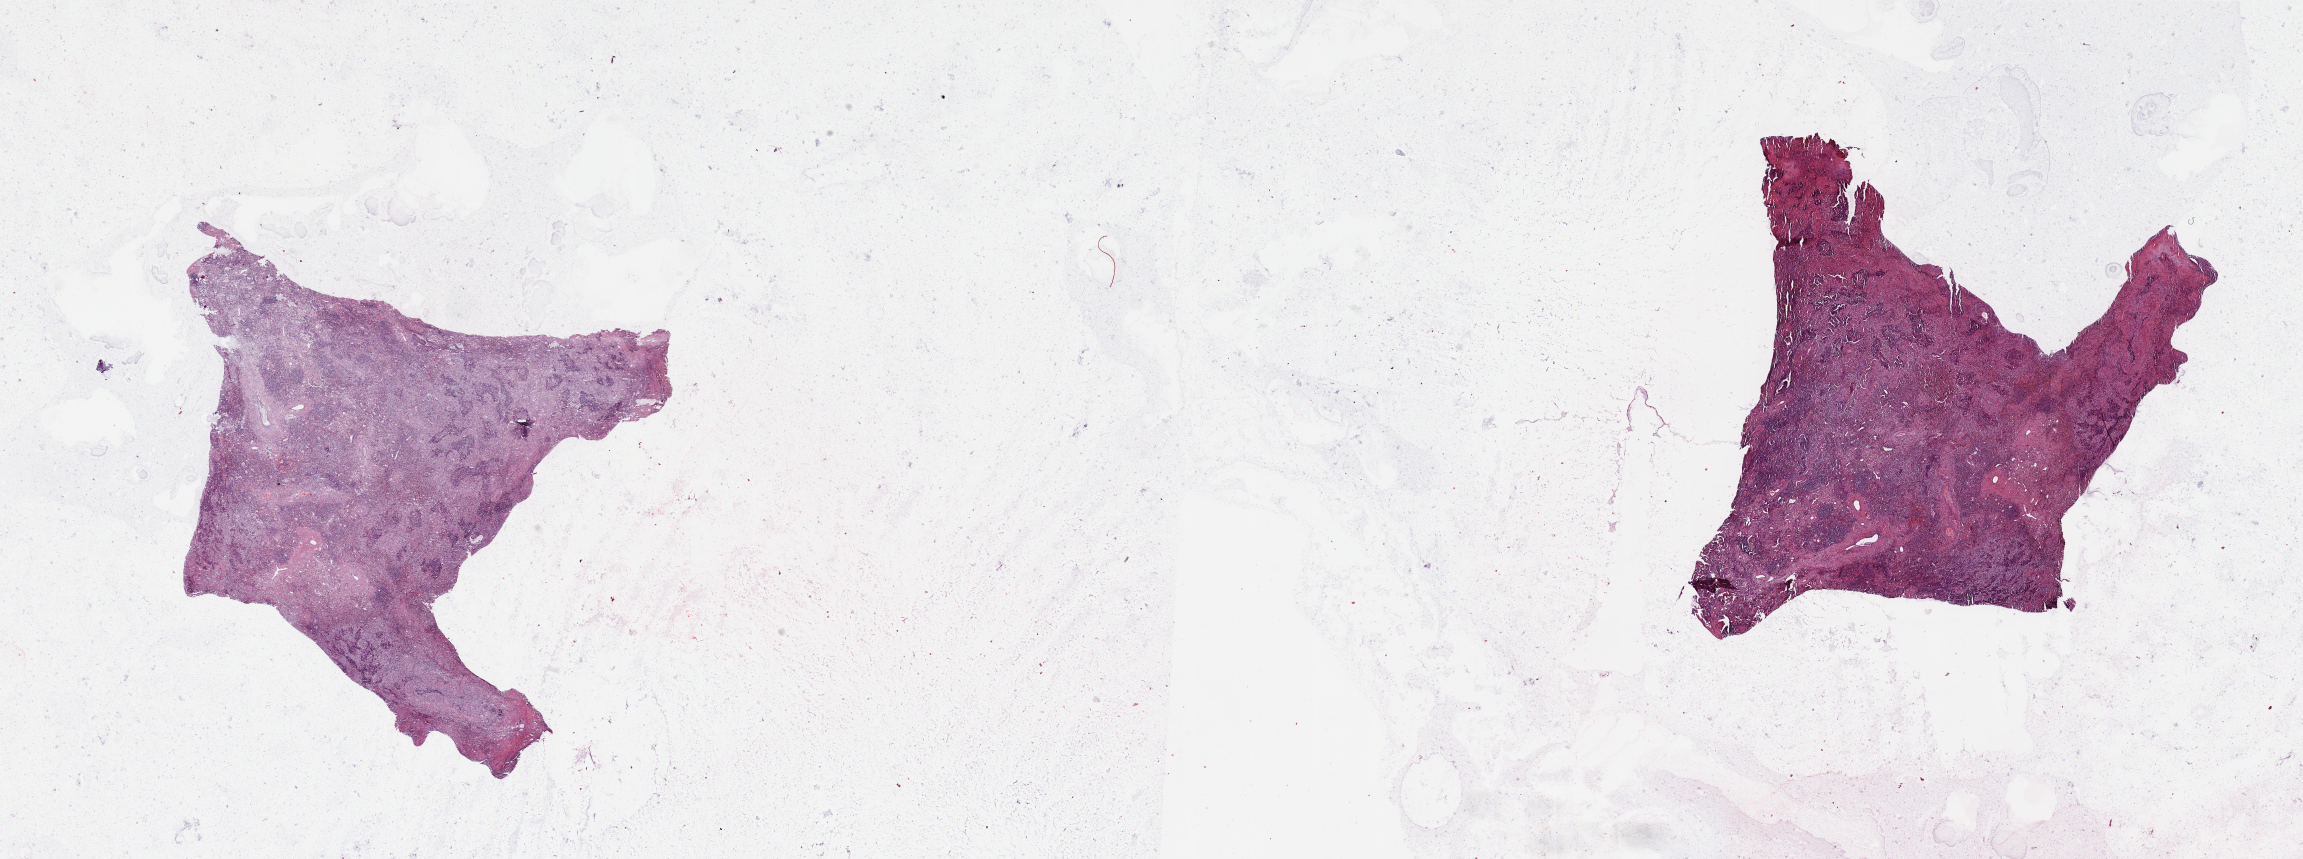
Digitized H&E-stained tissue section (whole slide), whole scanned area (about 36.4 x 13.6 mm, slide scanned at 20x) shown as a low-resolution overview. Tumour tissue sample, lung. Male, 72 y/o. Histologic grade: G3 (poorly differentiated).
AJCC pathologic stage: IIIA. Histologic diagnosis: Squamous cell carcinoma, NOS.